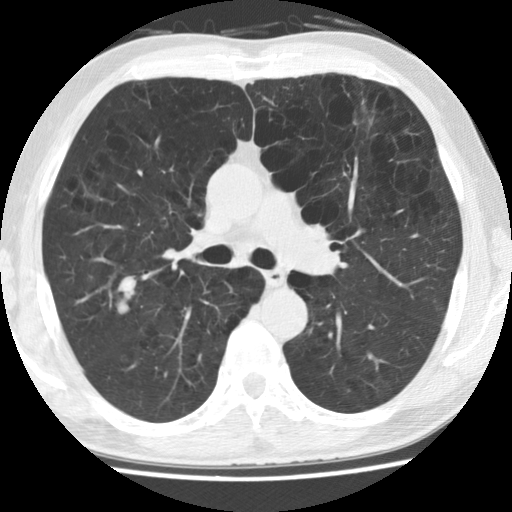
Low-dose screening chest CT, one axial slice. Position 94 of 158 along the scan axis. Reconstruction kernel STANDARD. 120 kVp. Lung window (W 1500 / L -600 HU). 2.5 mm slice thickness. 512 × 512 image matrix.
Structures marked on this image (expert manual segmentation):
- lesion 1 (tumor, upper lobe of right lung): box from (x=117, y=292) to (x=133, y=314) px